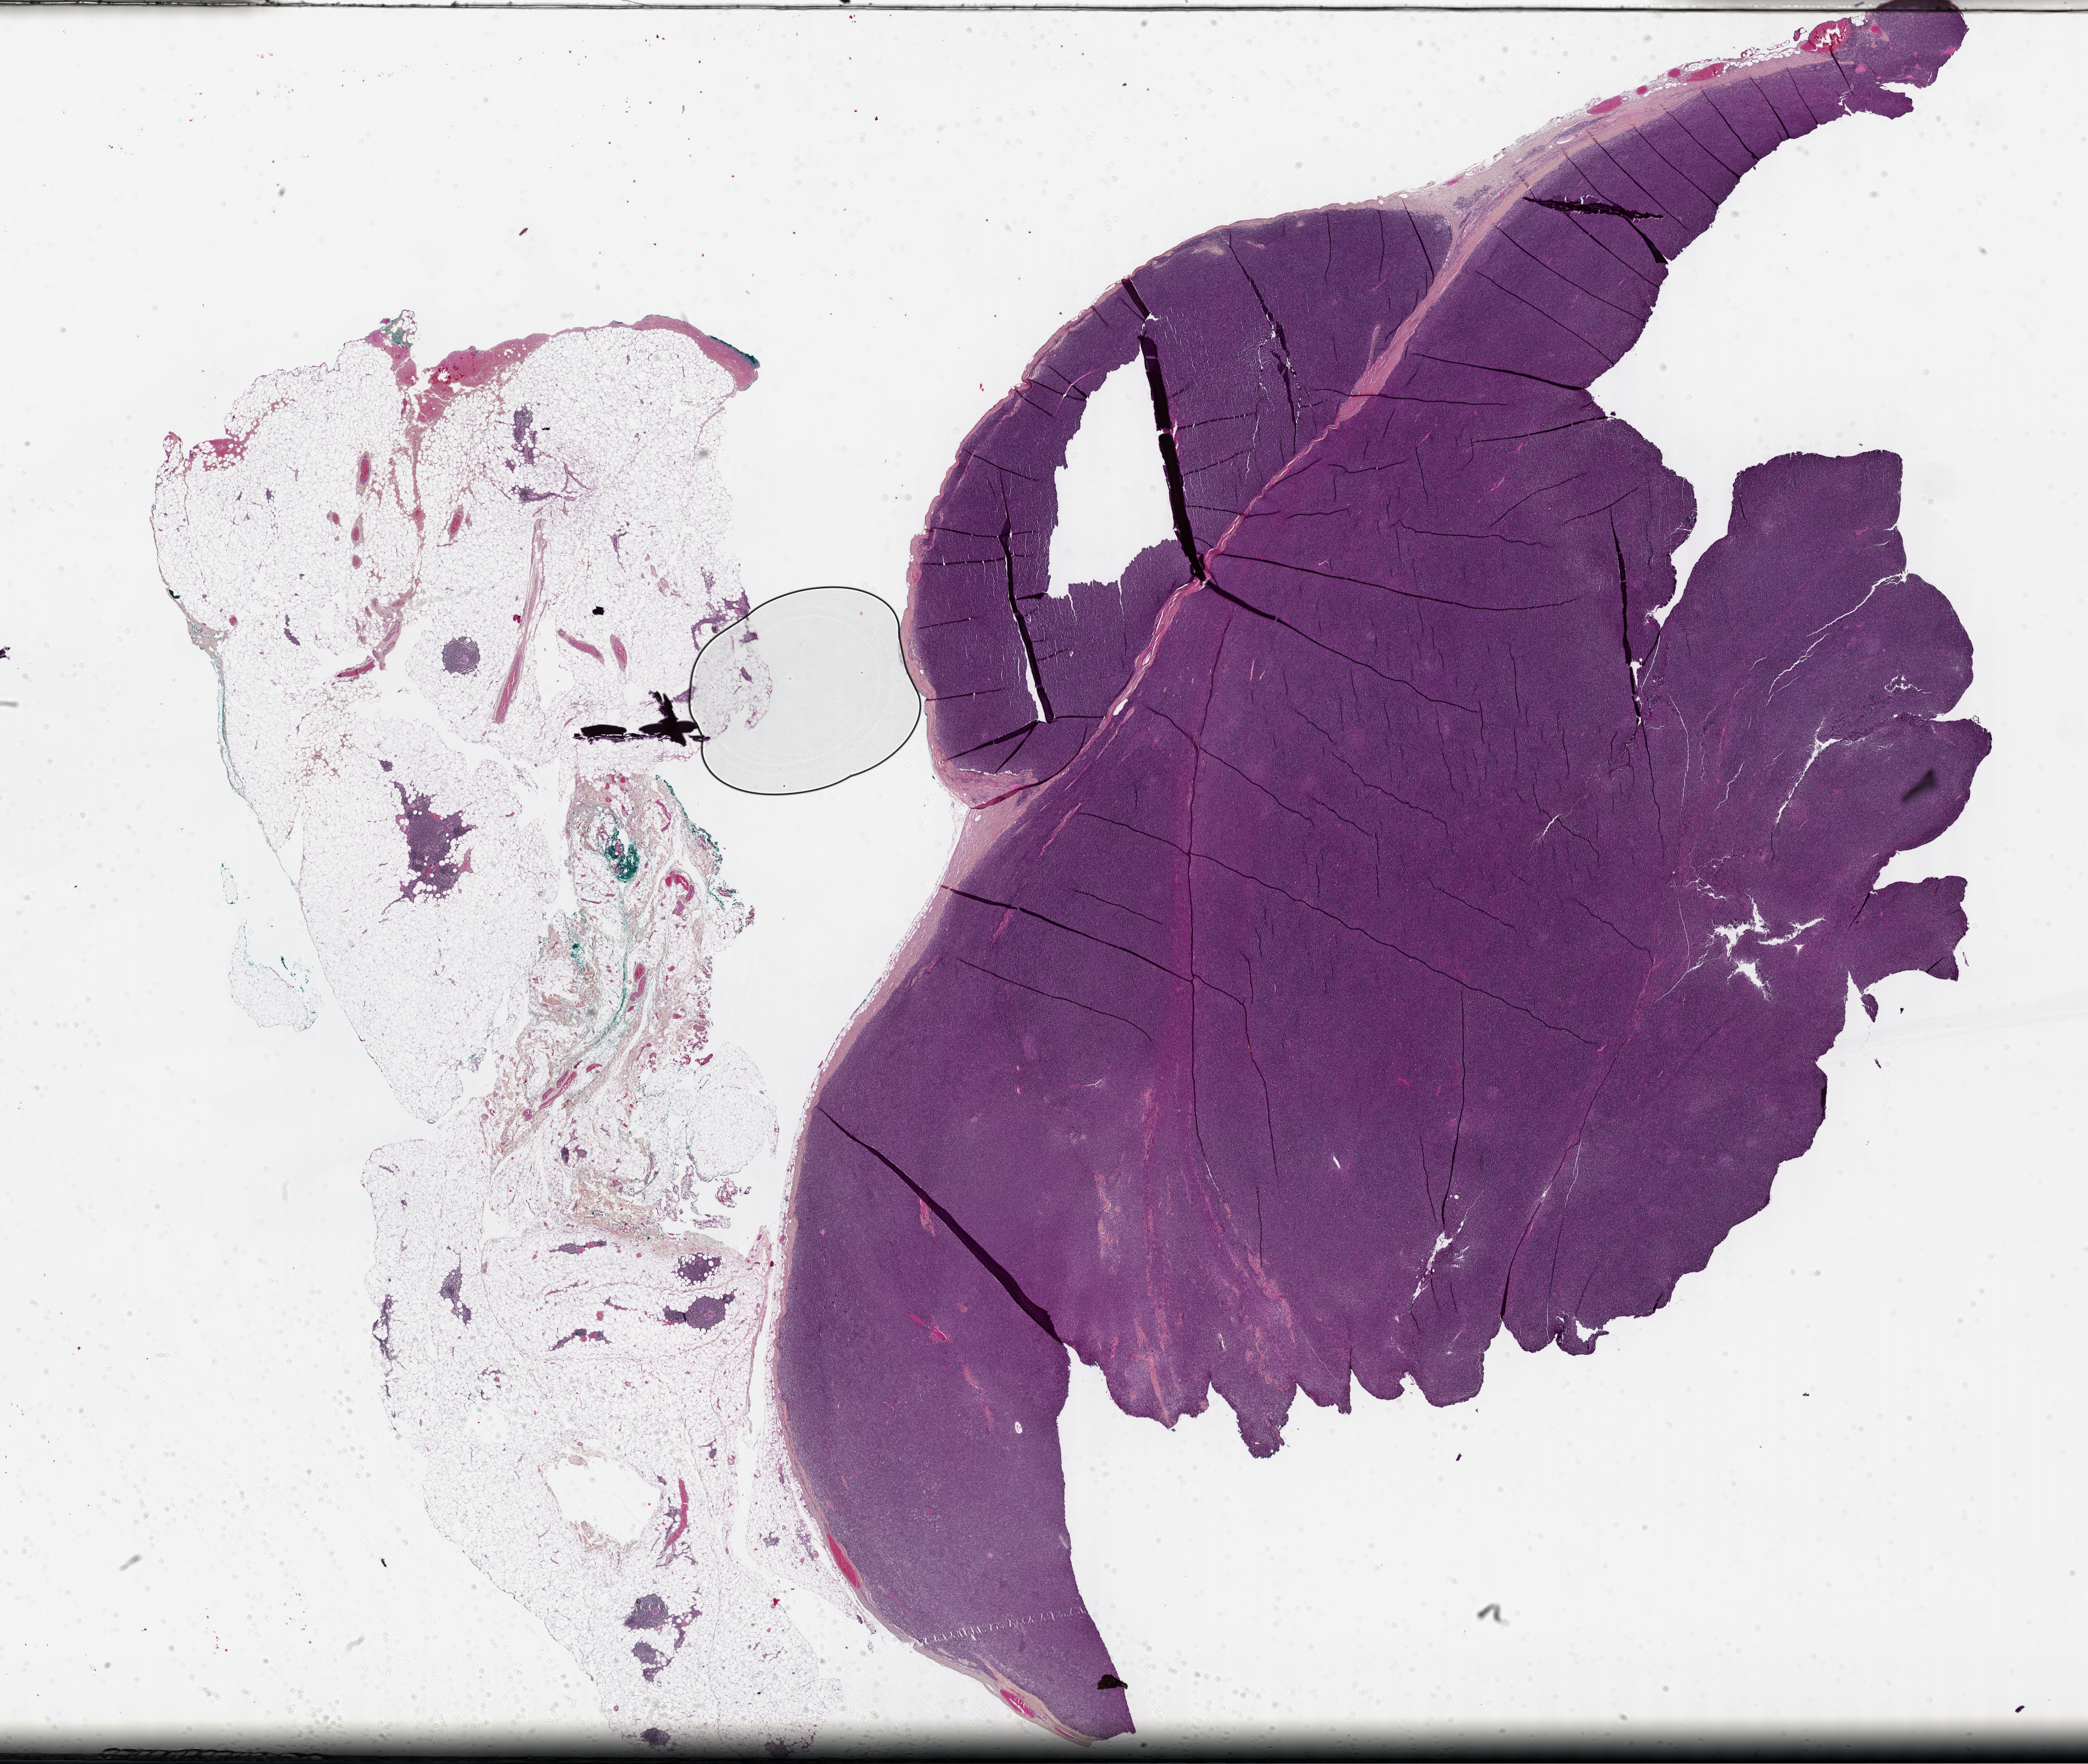
Digitized H&E-stained tissue section (whole slide) — shown as a low-resolution overview of the whole scanned area (about 28.2 x 23.8 mm, slide scanned at 40x), FFPE section, primary tumour sample from the thymus. Male patient; age at initial diagnosis 62 years.
Pathologic diagnosis: Thymoma, type AB, malignant.